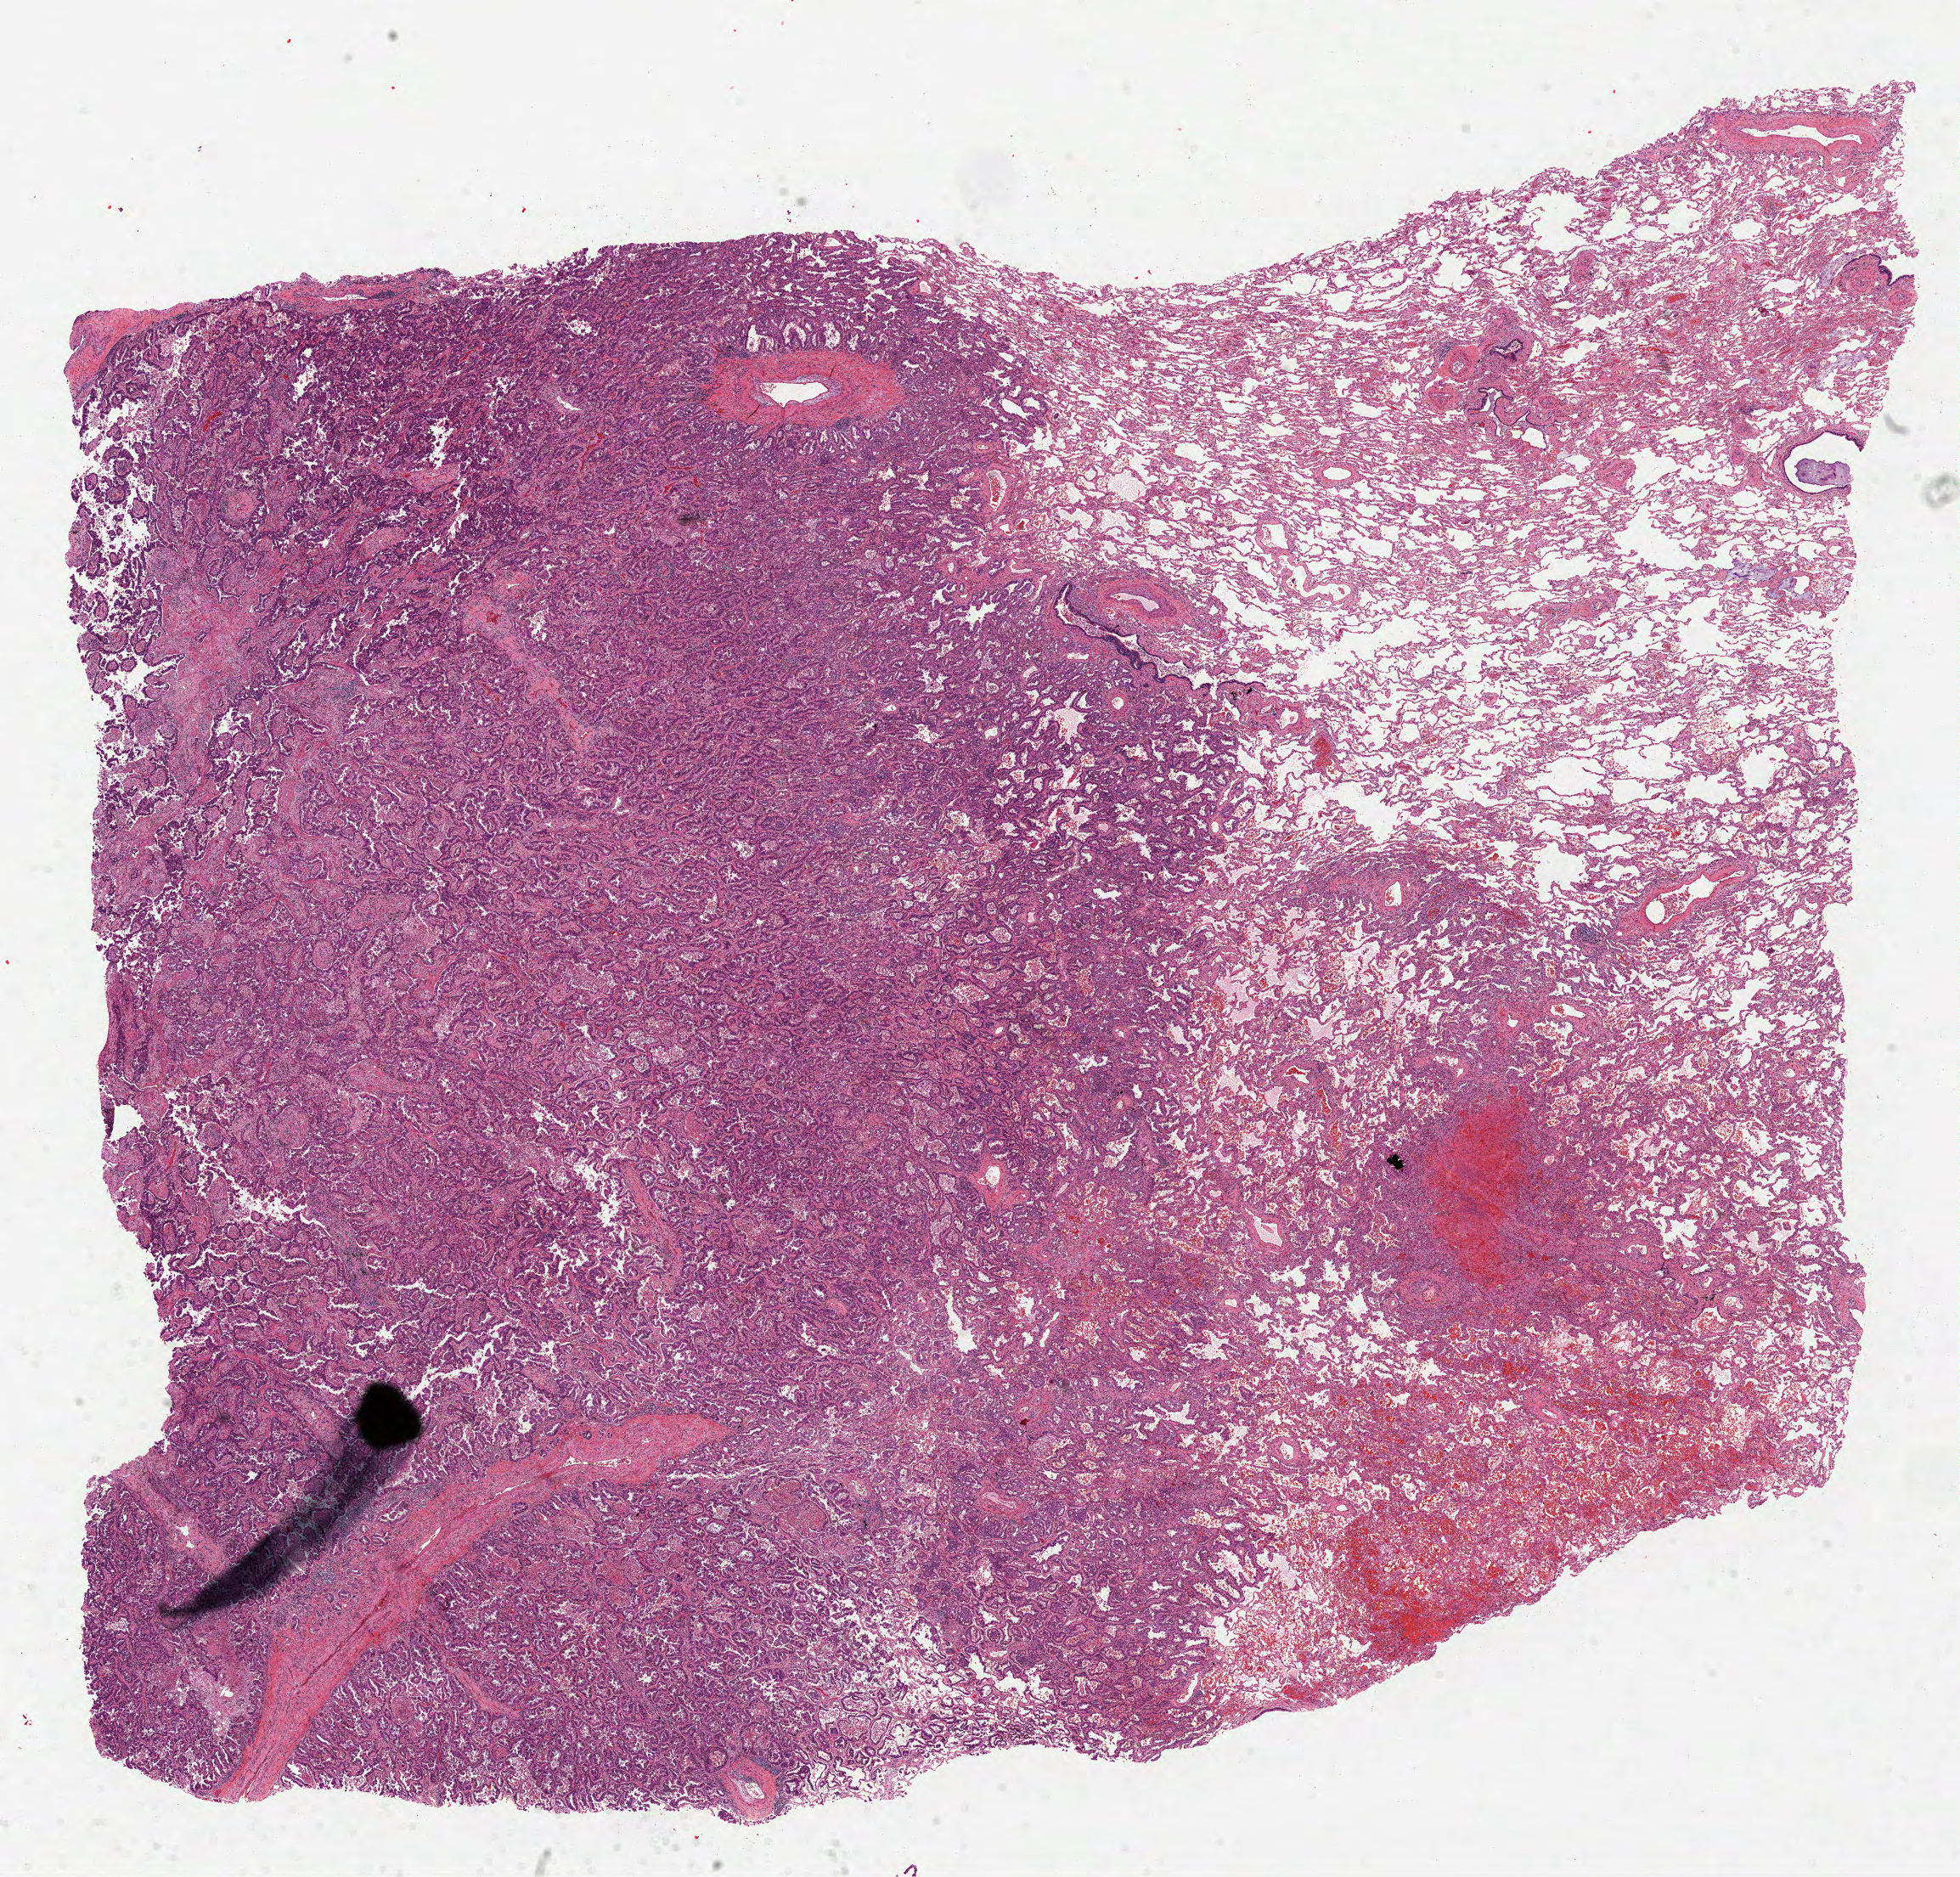
H&E-stained whole-slide image, low-resolution overview of the scanned area, about 18.6 x 17.8 mm, formalin-fixed paraffin-embedded (FFPE) diagnostic section, lung, primary tumour sample. Patient: male, age at initial diagnosis 73 years.
Laterality: right. Diagnosis: Adenocarcinoma with mixed subtypes (lower lobe, lung). AJCC pathologic stage: IIB (7th edition).